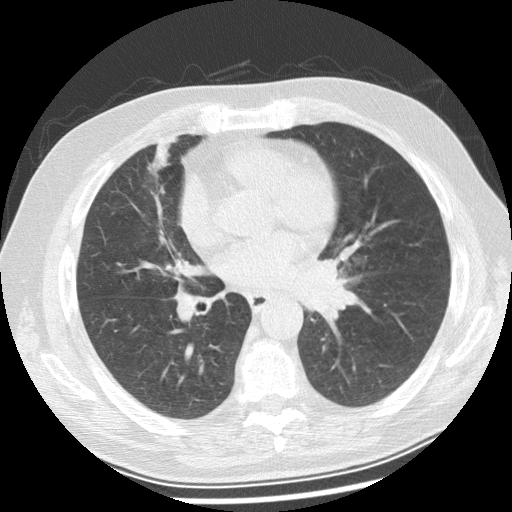
Low-dose screening chest CT, axial slice; first (baseline) screen; lung window (W 1500 / L -600 HU). Male participant, aged 70 years at enrolment. Current smoker at enrolment.
Lesion marked by an expert reader, bounding box (x1, y1, x2, y2) in pixels: (293, 240, 377, 325). No non-calcified nodule or mass ≥4 mm was recorded by the screening reader at this exam. Official screen result: positive, change unspecified: nodule(s) >= 4 mm or enlarging nodule(s), mass(es), or other non-specific abnormalities suspicious for lung cancer. Participant outcome: lung cancer diagnosed 29 days after this screen — squamous cell carcinoma, keratinizing, NOS, left main stem bronchus, moderately differentiated (G2), stage IIIB (AJCC 6th edition), 40 mm at pathology.